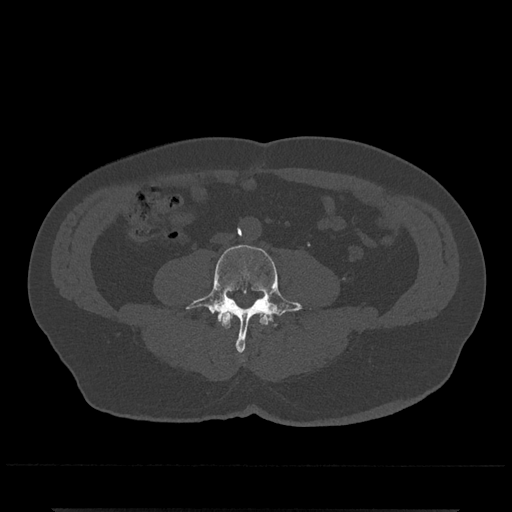
CT including the spine, one axial slice. Slice 159 of 797 in the series (ordered by position). Bone window (W 1800 / L 400 HU). 0.5 mm slice thickness. 512 × 512 image matrix, field of view 393 × 393 mm. Male patient, age 67 years. From the clinical record (not read from this slice): primary cancer: prostate.
Annotated regions visible in this slice (semi-automatic segmentation, software-assisted and operator-edited):
- L3 vertebra: box from (x=220, y=310) to (x=270, y=328) px
- L4 vertebra: (x=186, y=244)–(x=312, y=352)